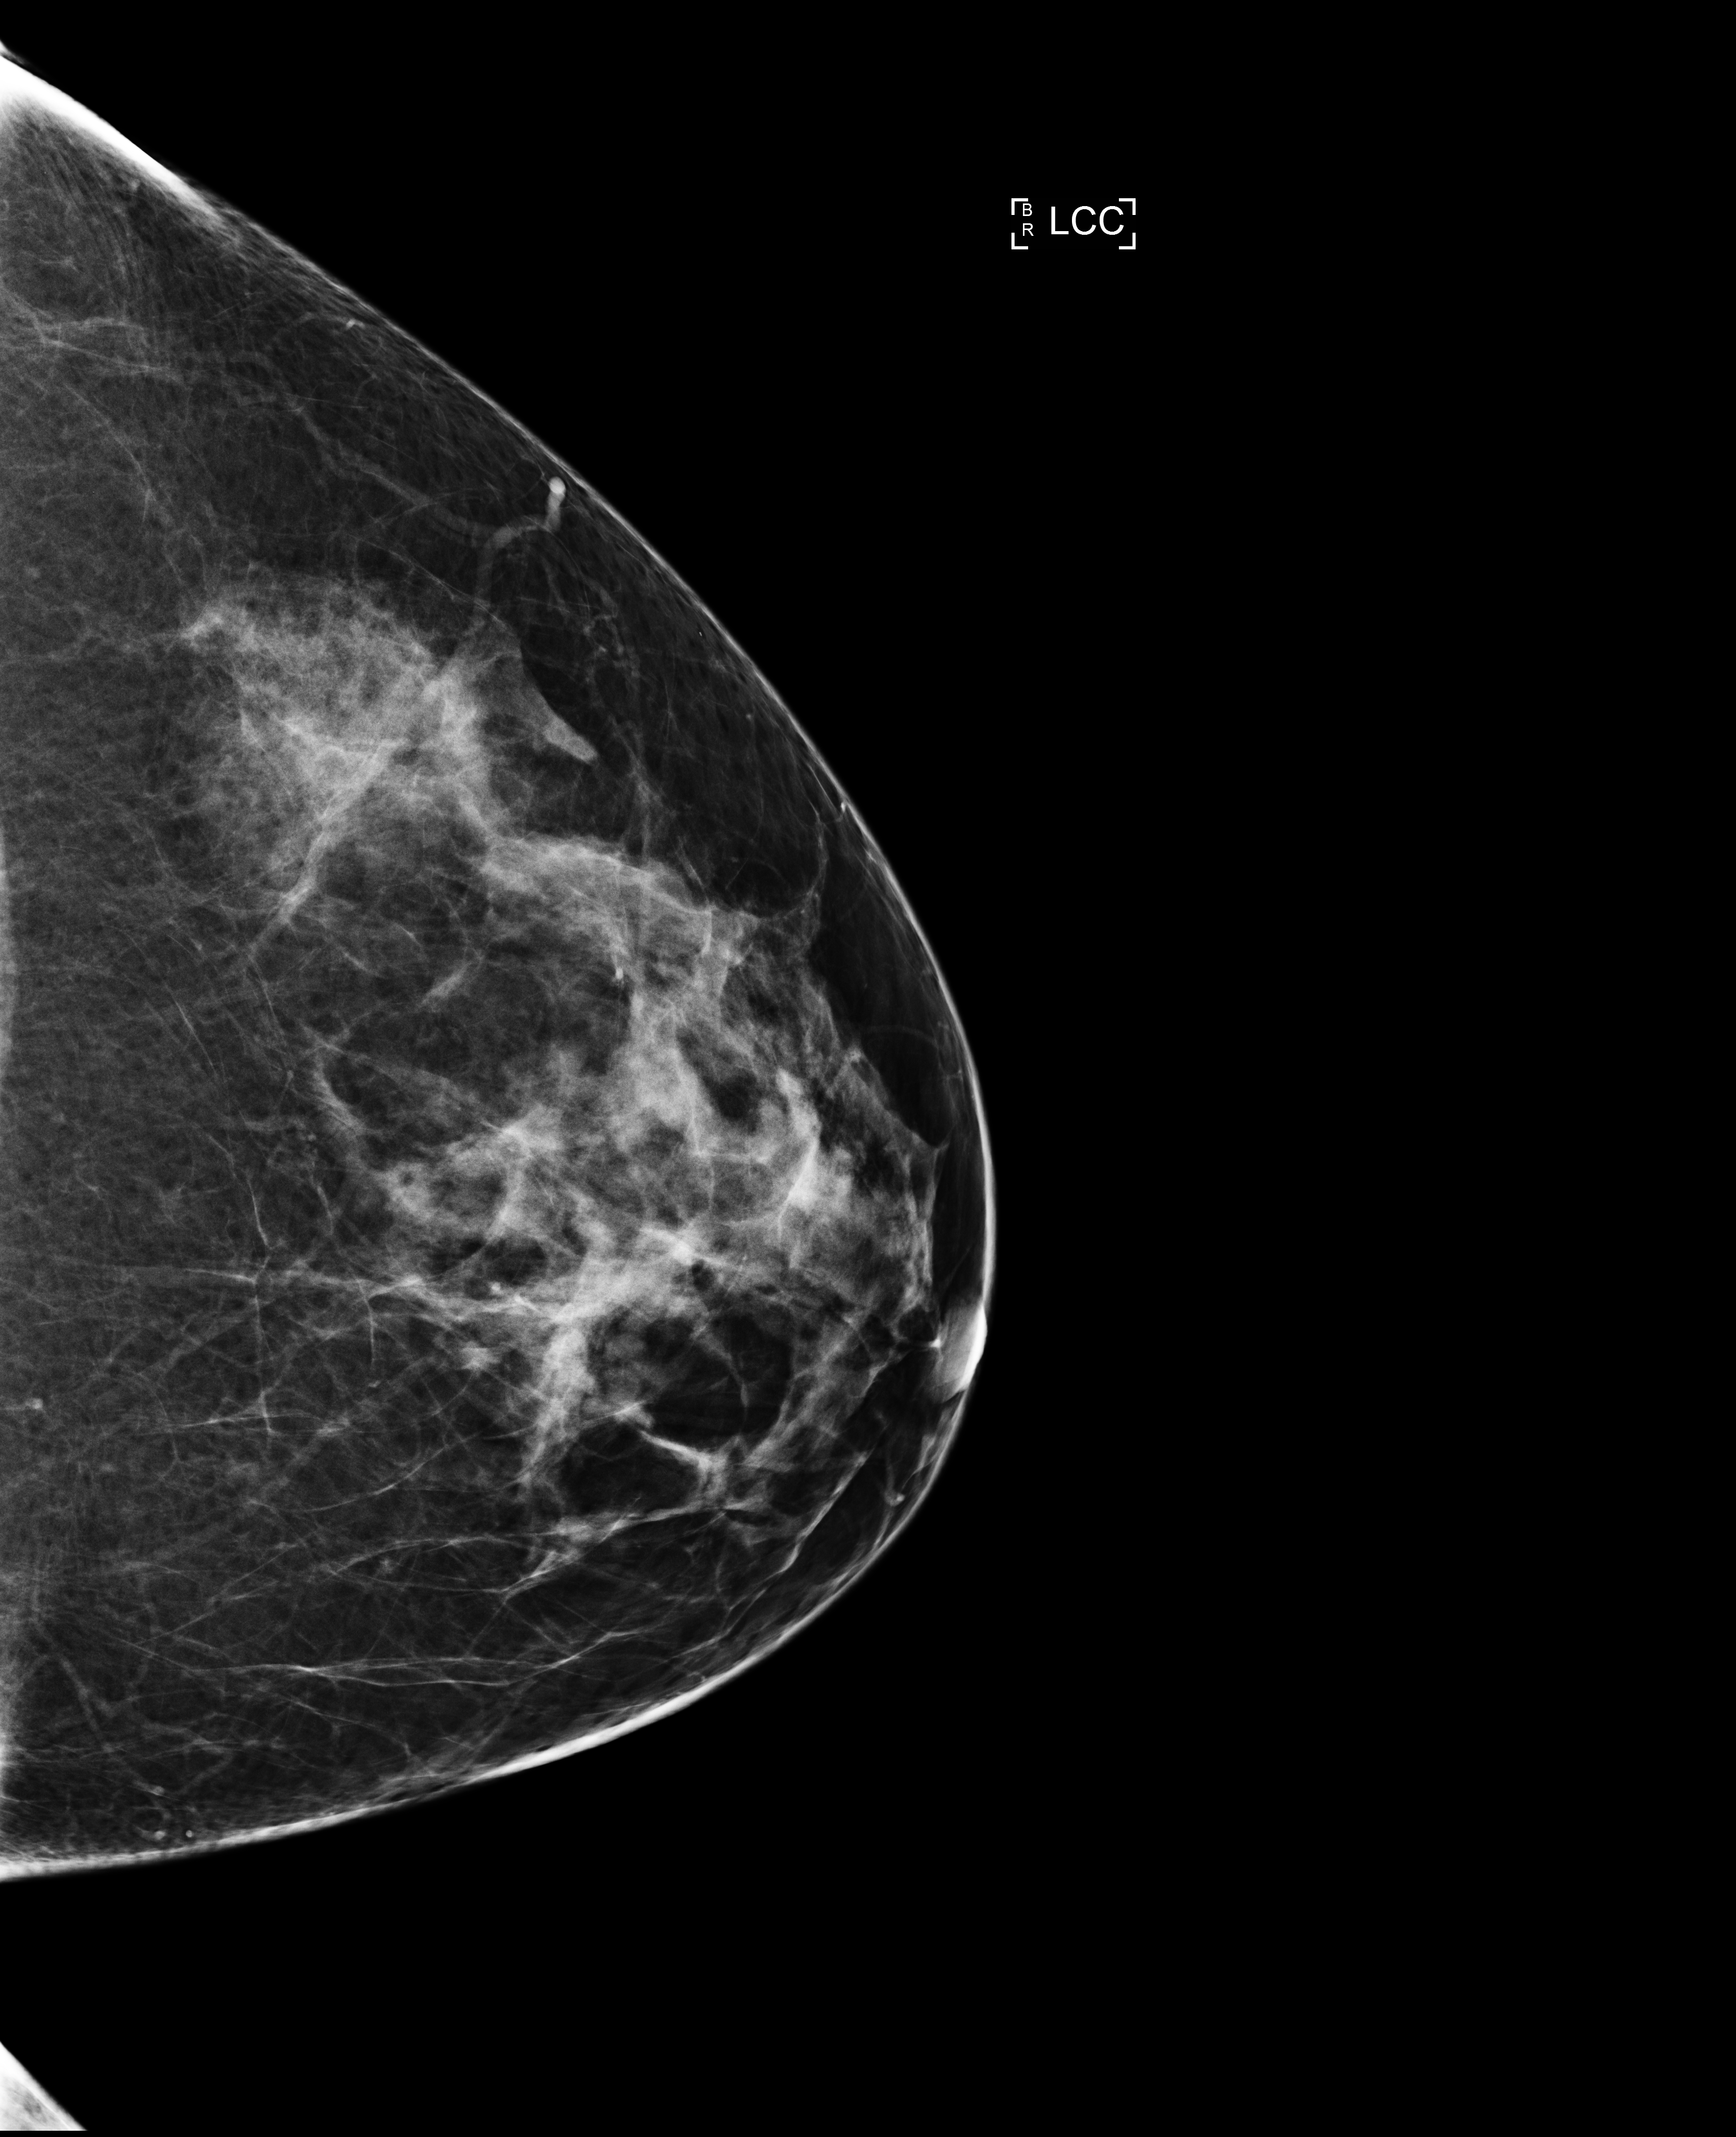
Screening examination. Patient aged 46 years (female).
Image type: full-field digital mammogram. Breast: left. Projection: cranio-caudal projection.